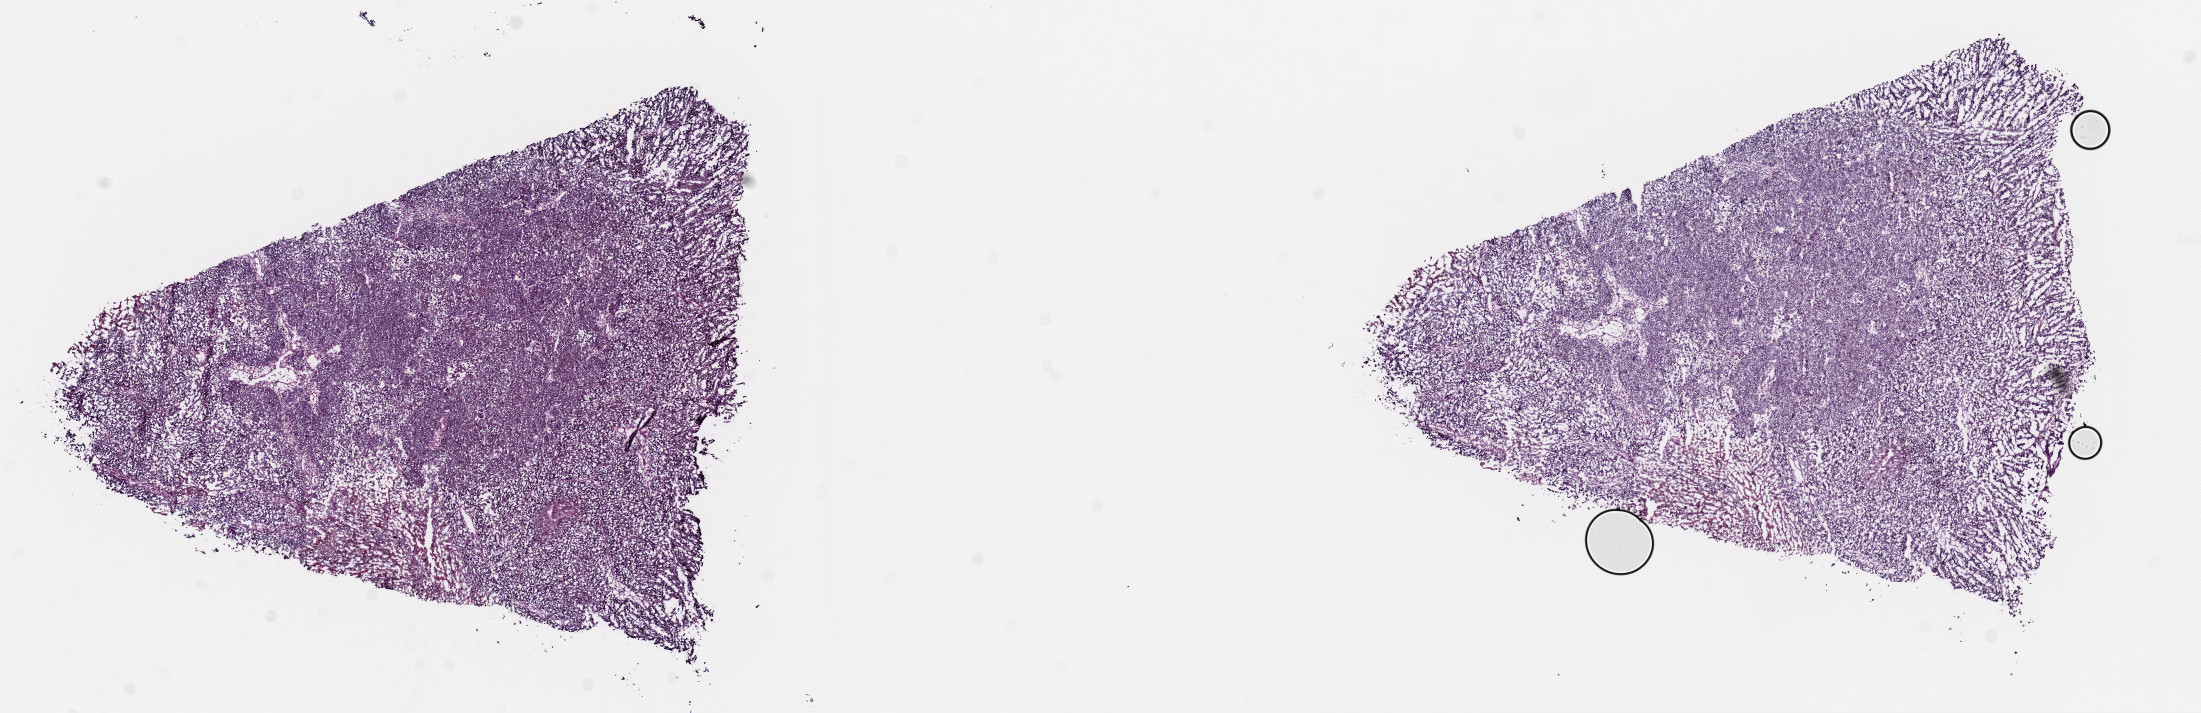
Whole-slide histology image, Hematoxylin and eosin (H&E) stained — whole scanned area (about 17.4 x 5.6 mm) shown as a low-resolution overview; frozen section from the top of the tissue portion; metastatic tumour sample, sampled site: lymph nodes of axilla or arm. Male patient; age at initial diagnosis 54 years. Composition of this section per pathologist review: tumour cells 90%, tumour nuclei 90%, normal cells 0%, stromal cells 10%, necrosis 0%. Infiltration values recorded for this section: lymphocyte infiltration 2%, monocyte infiltration 1%, neutrophil infiltration 0%.
This section: metastatic tumour tissue. Patient diagnosis: Malignant melanoma, NOS.